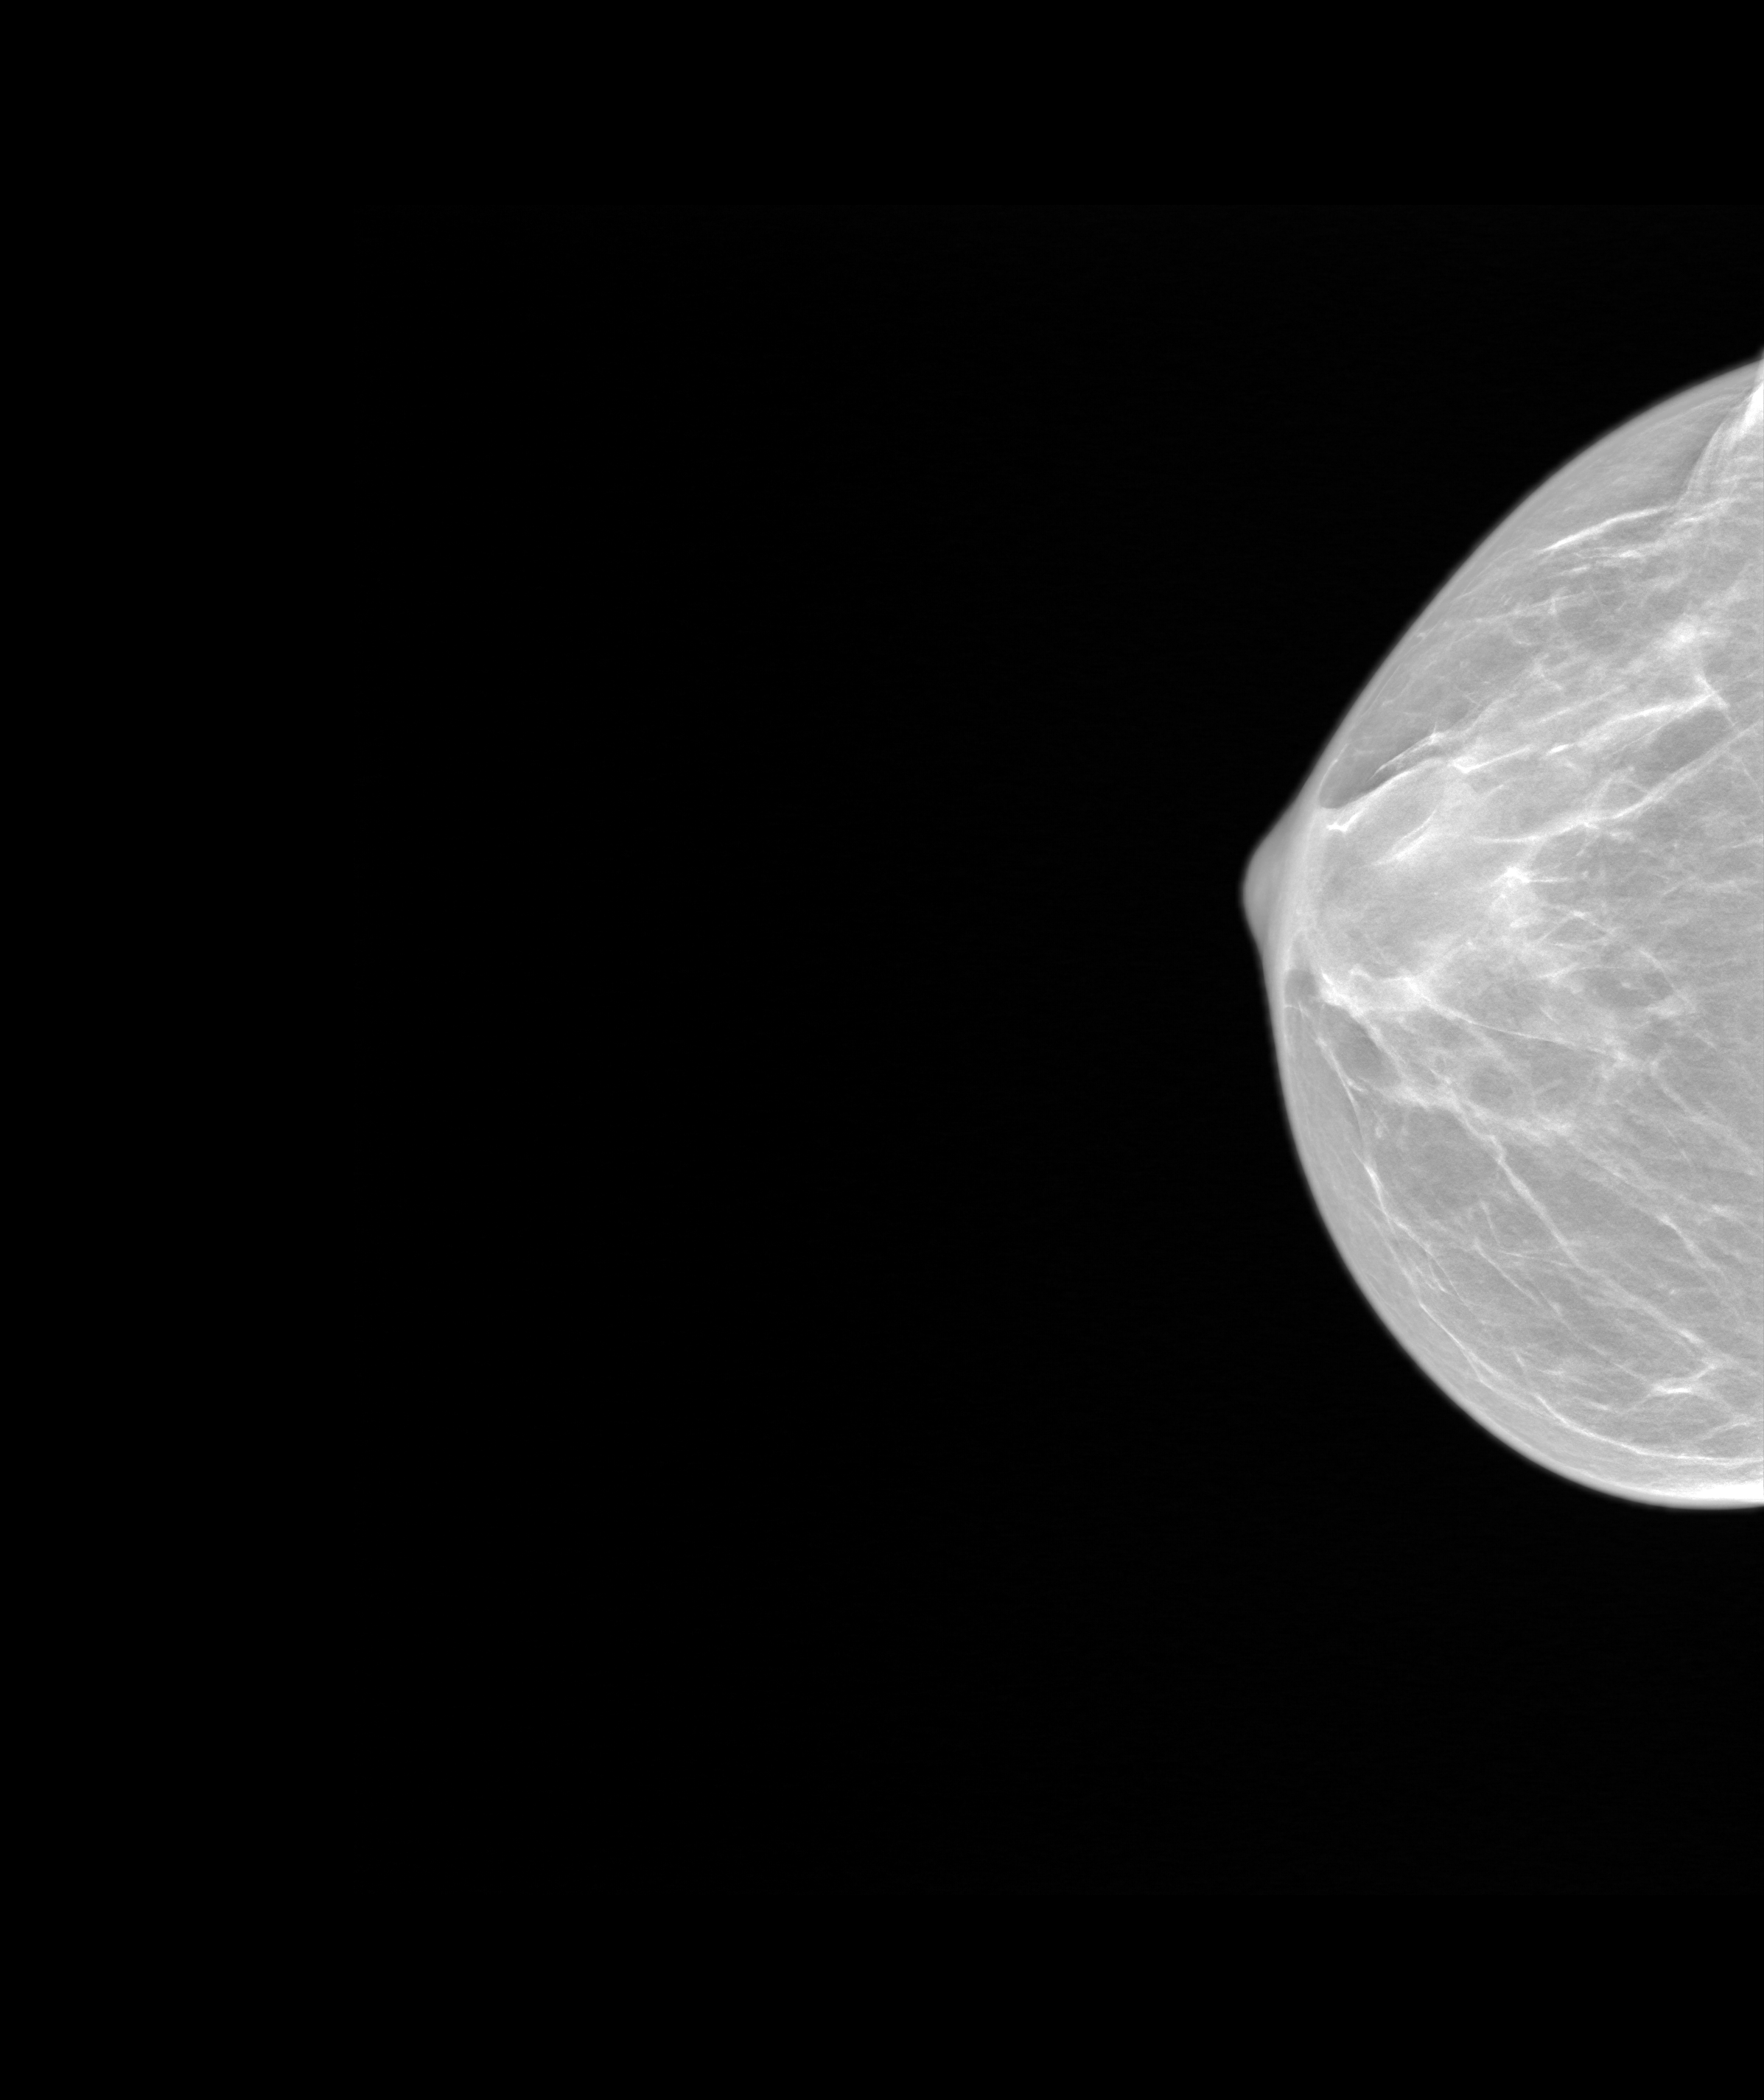
Annual screening mammography examination. Patient: female, 66 years.
Image type: synthesized 2-D view from tomosynthesis. Breast: right. Projection: craniocaudal (CC) view.